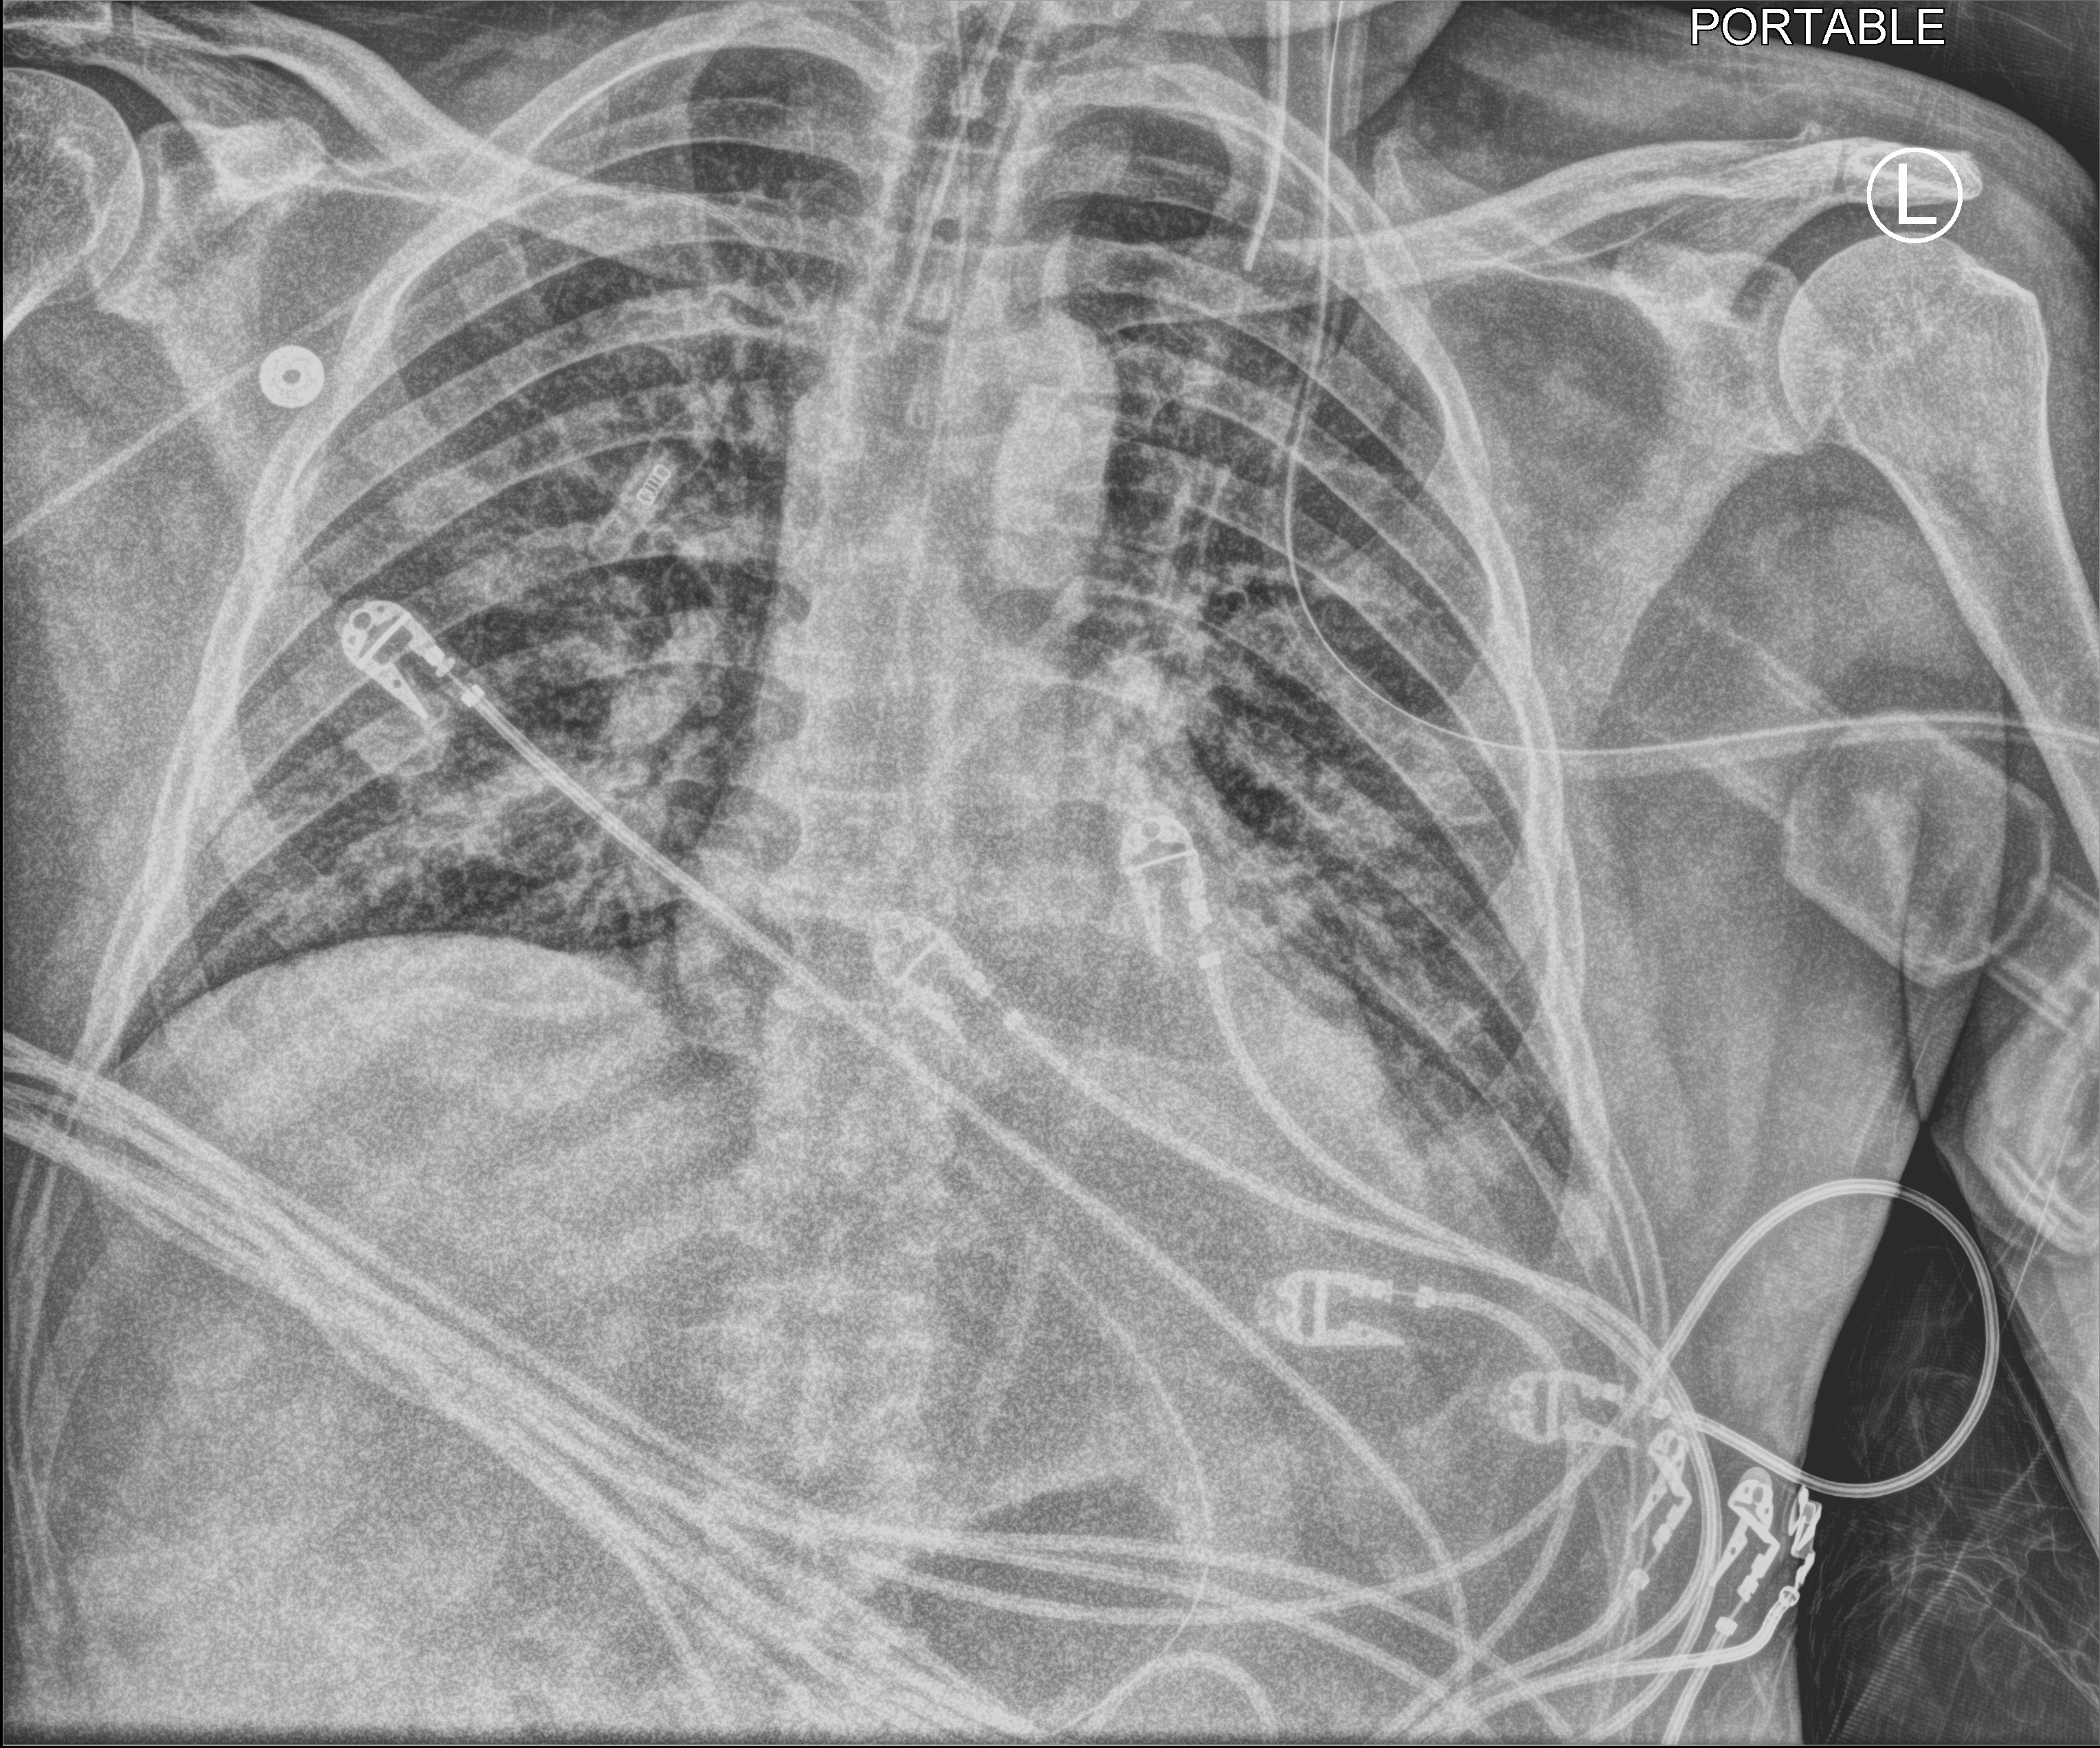
Portable chest radiograph; anteroposterior (AP) projection. Male patient hospitalised with COVID-19, age 18–59 years.
From the hospital-stay record, not from the radiograph (when in the stay this image was taken is not recorded): length of hospital stay: 83 days; diabetes (admission record): no; admitted to intensive care during this hospital stay: yes.